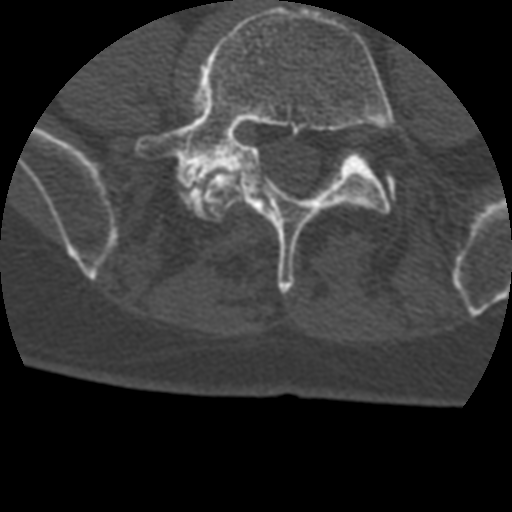
CT including the spine, one axial slice. Position 45 of 399 along the scan axis. Reconstruction kernel STANDARD. 120 kVp. Bone window (W 1800 / L 400 HU). 512 × 512 image matrix, field of view 160 × 160 mm. Patient age 69 years. From the clinical record (not read from this slice): primary cancer: prostate.
Outlined on this slice (semi-automatically segmented with operator editing):
- L4 vertebra: bounding box [x1, y1, x2, y2] px = [200, 171, 244, 220]
- L5 vertebra: [135, 6, 400, 293]